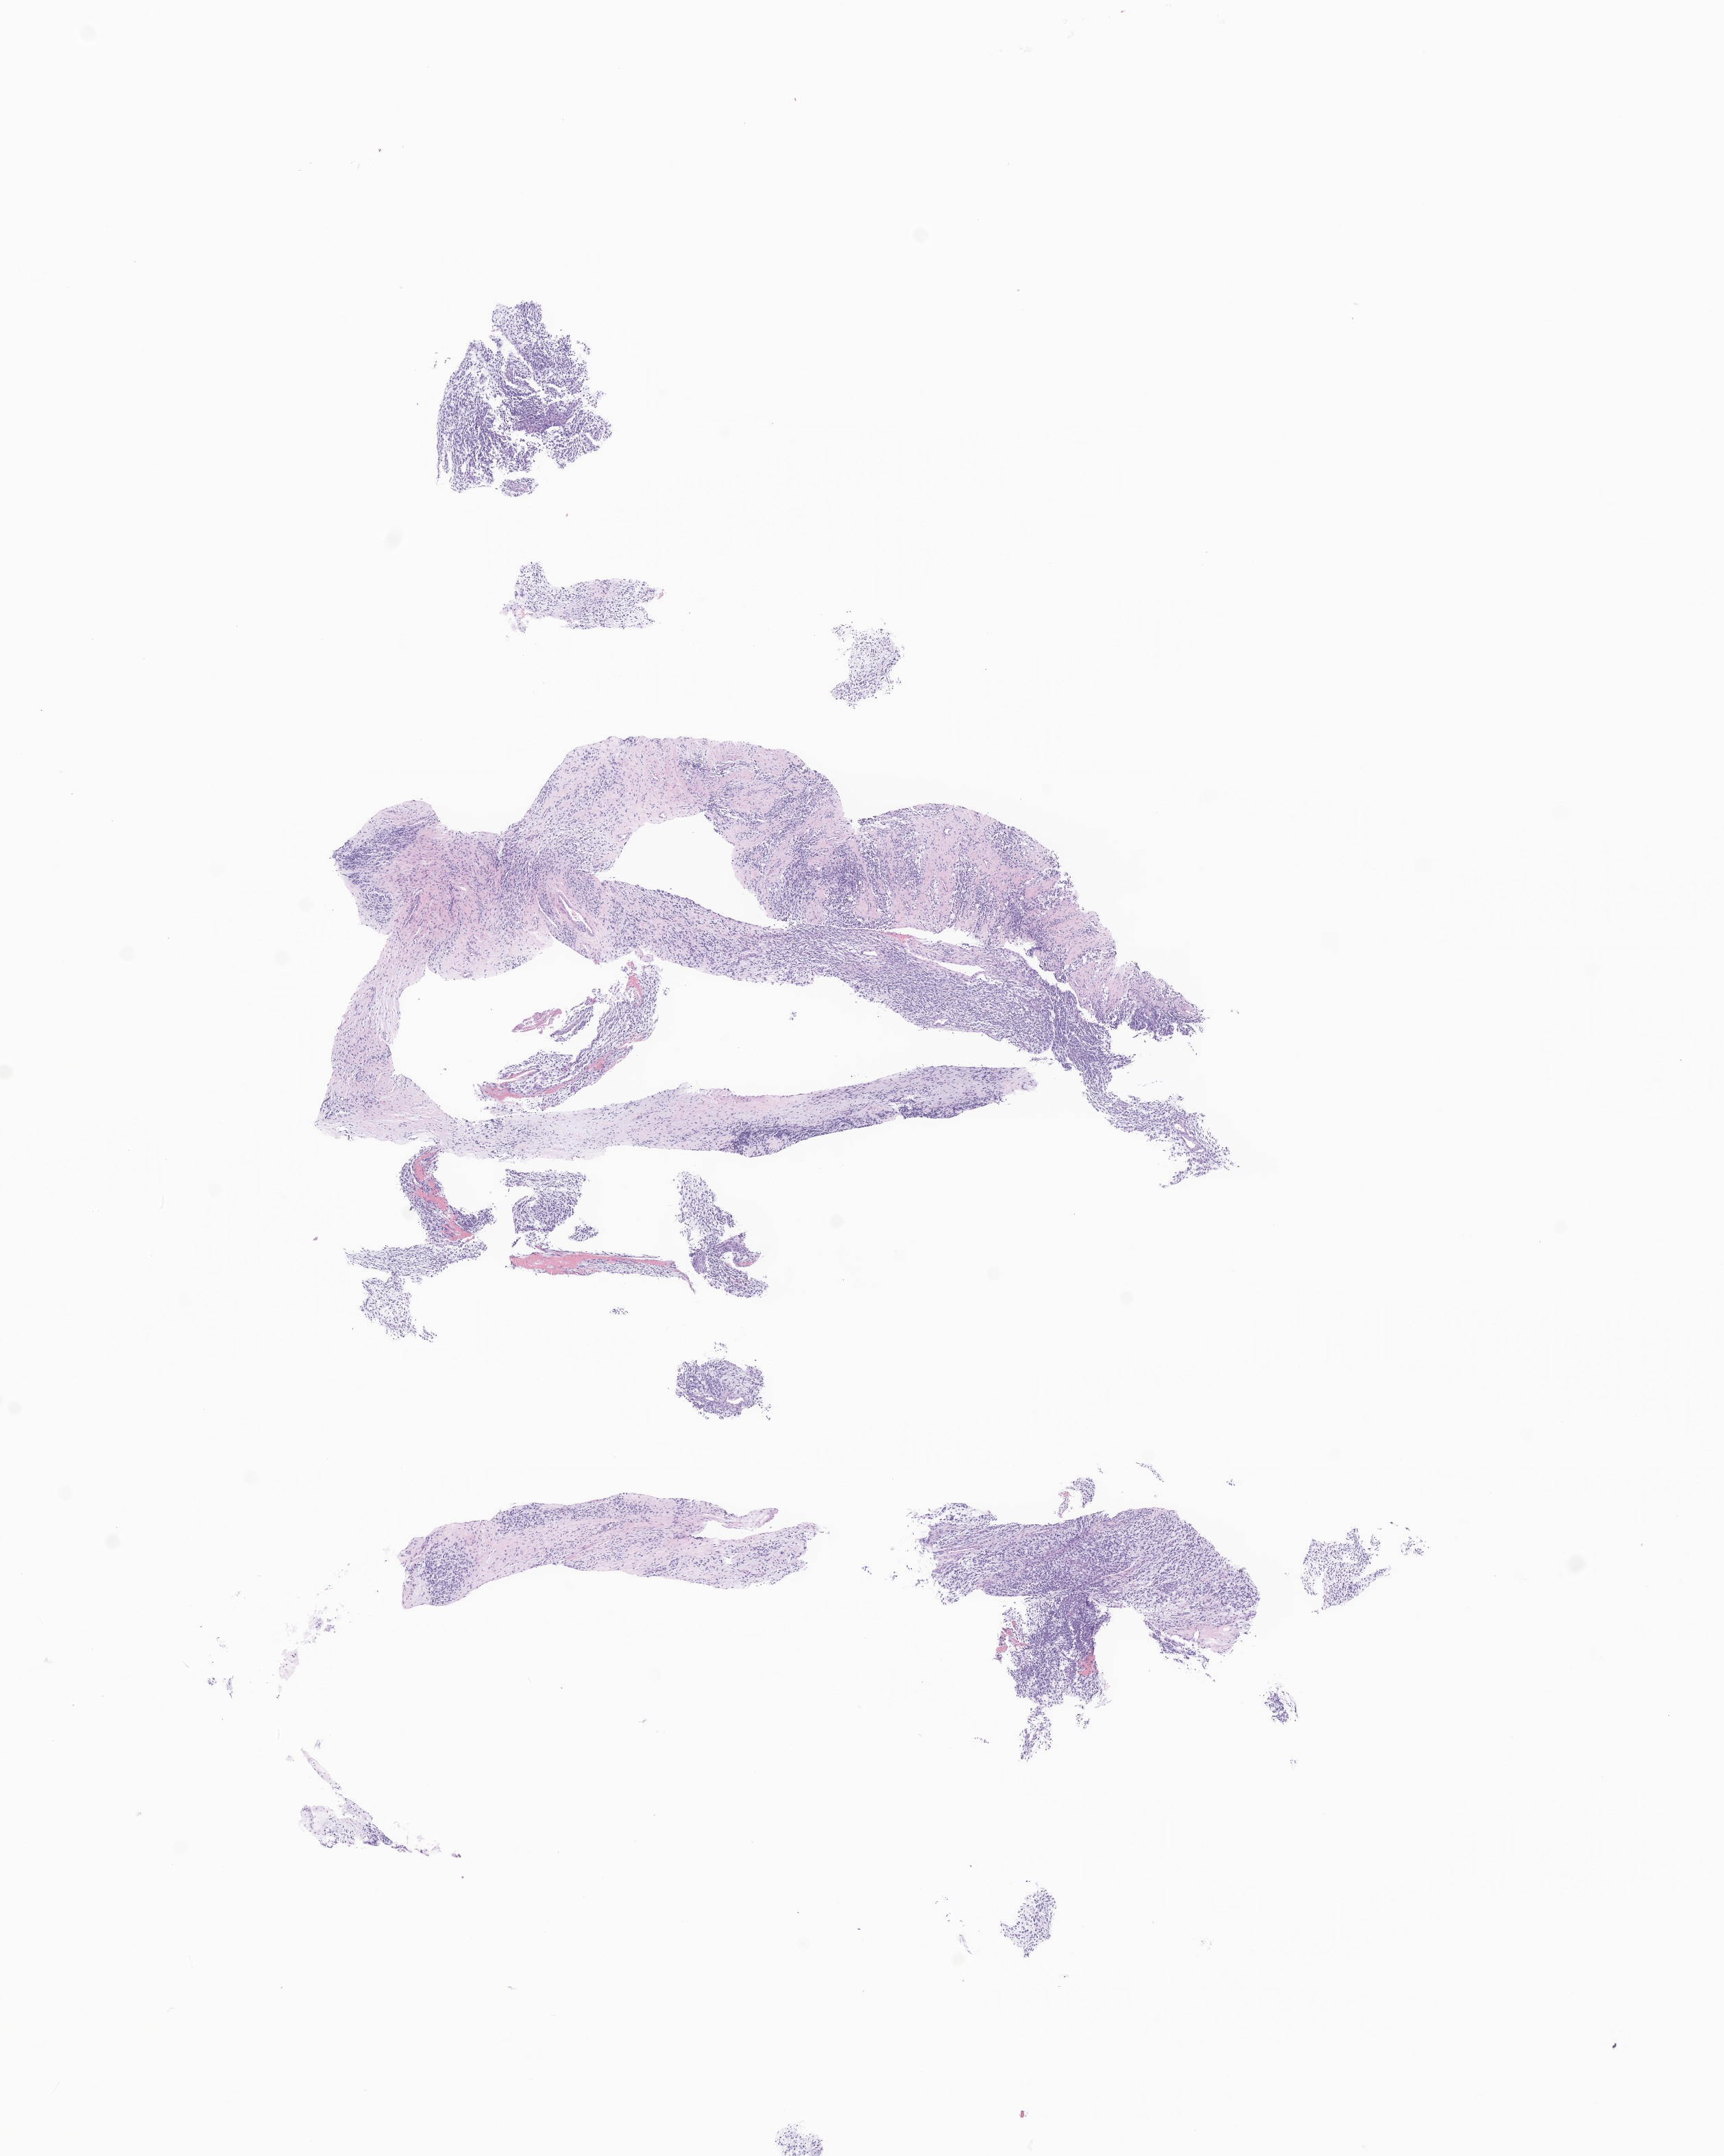
Digitized H&E-stained section of tumor tissue from the soft tissue of pelvis, a low-resolution overview of the entire scanned area, about 10.6 x 13.3 mm. Formalin-fixed paraffin-embedded section. Patient: male, age 34 months (2 years 10 months).
• diagnosis: Embryonal rhabdomyosarcoma, NOS